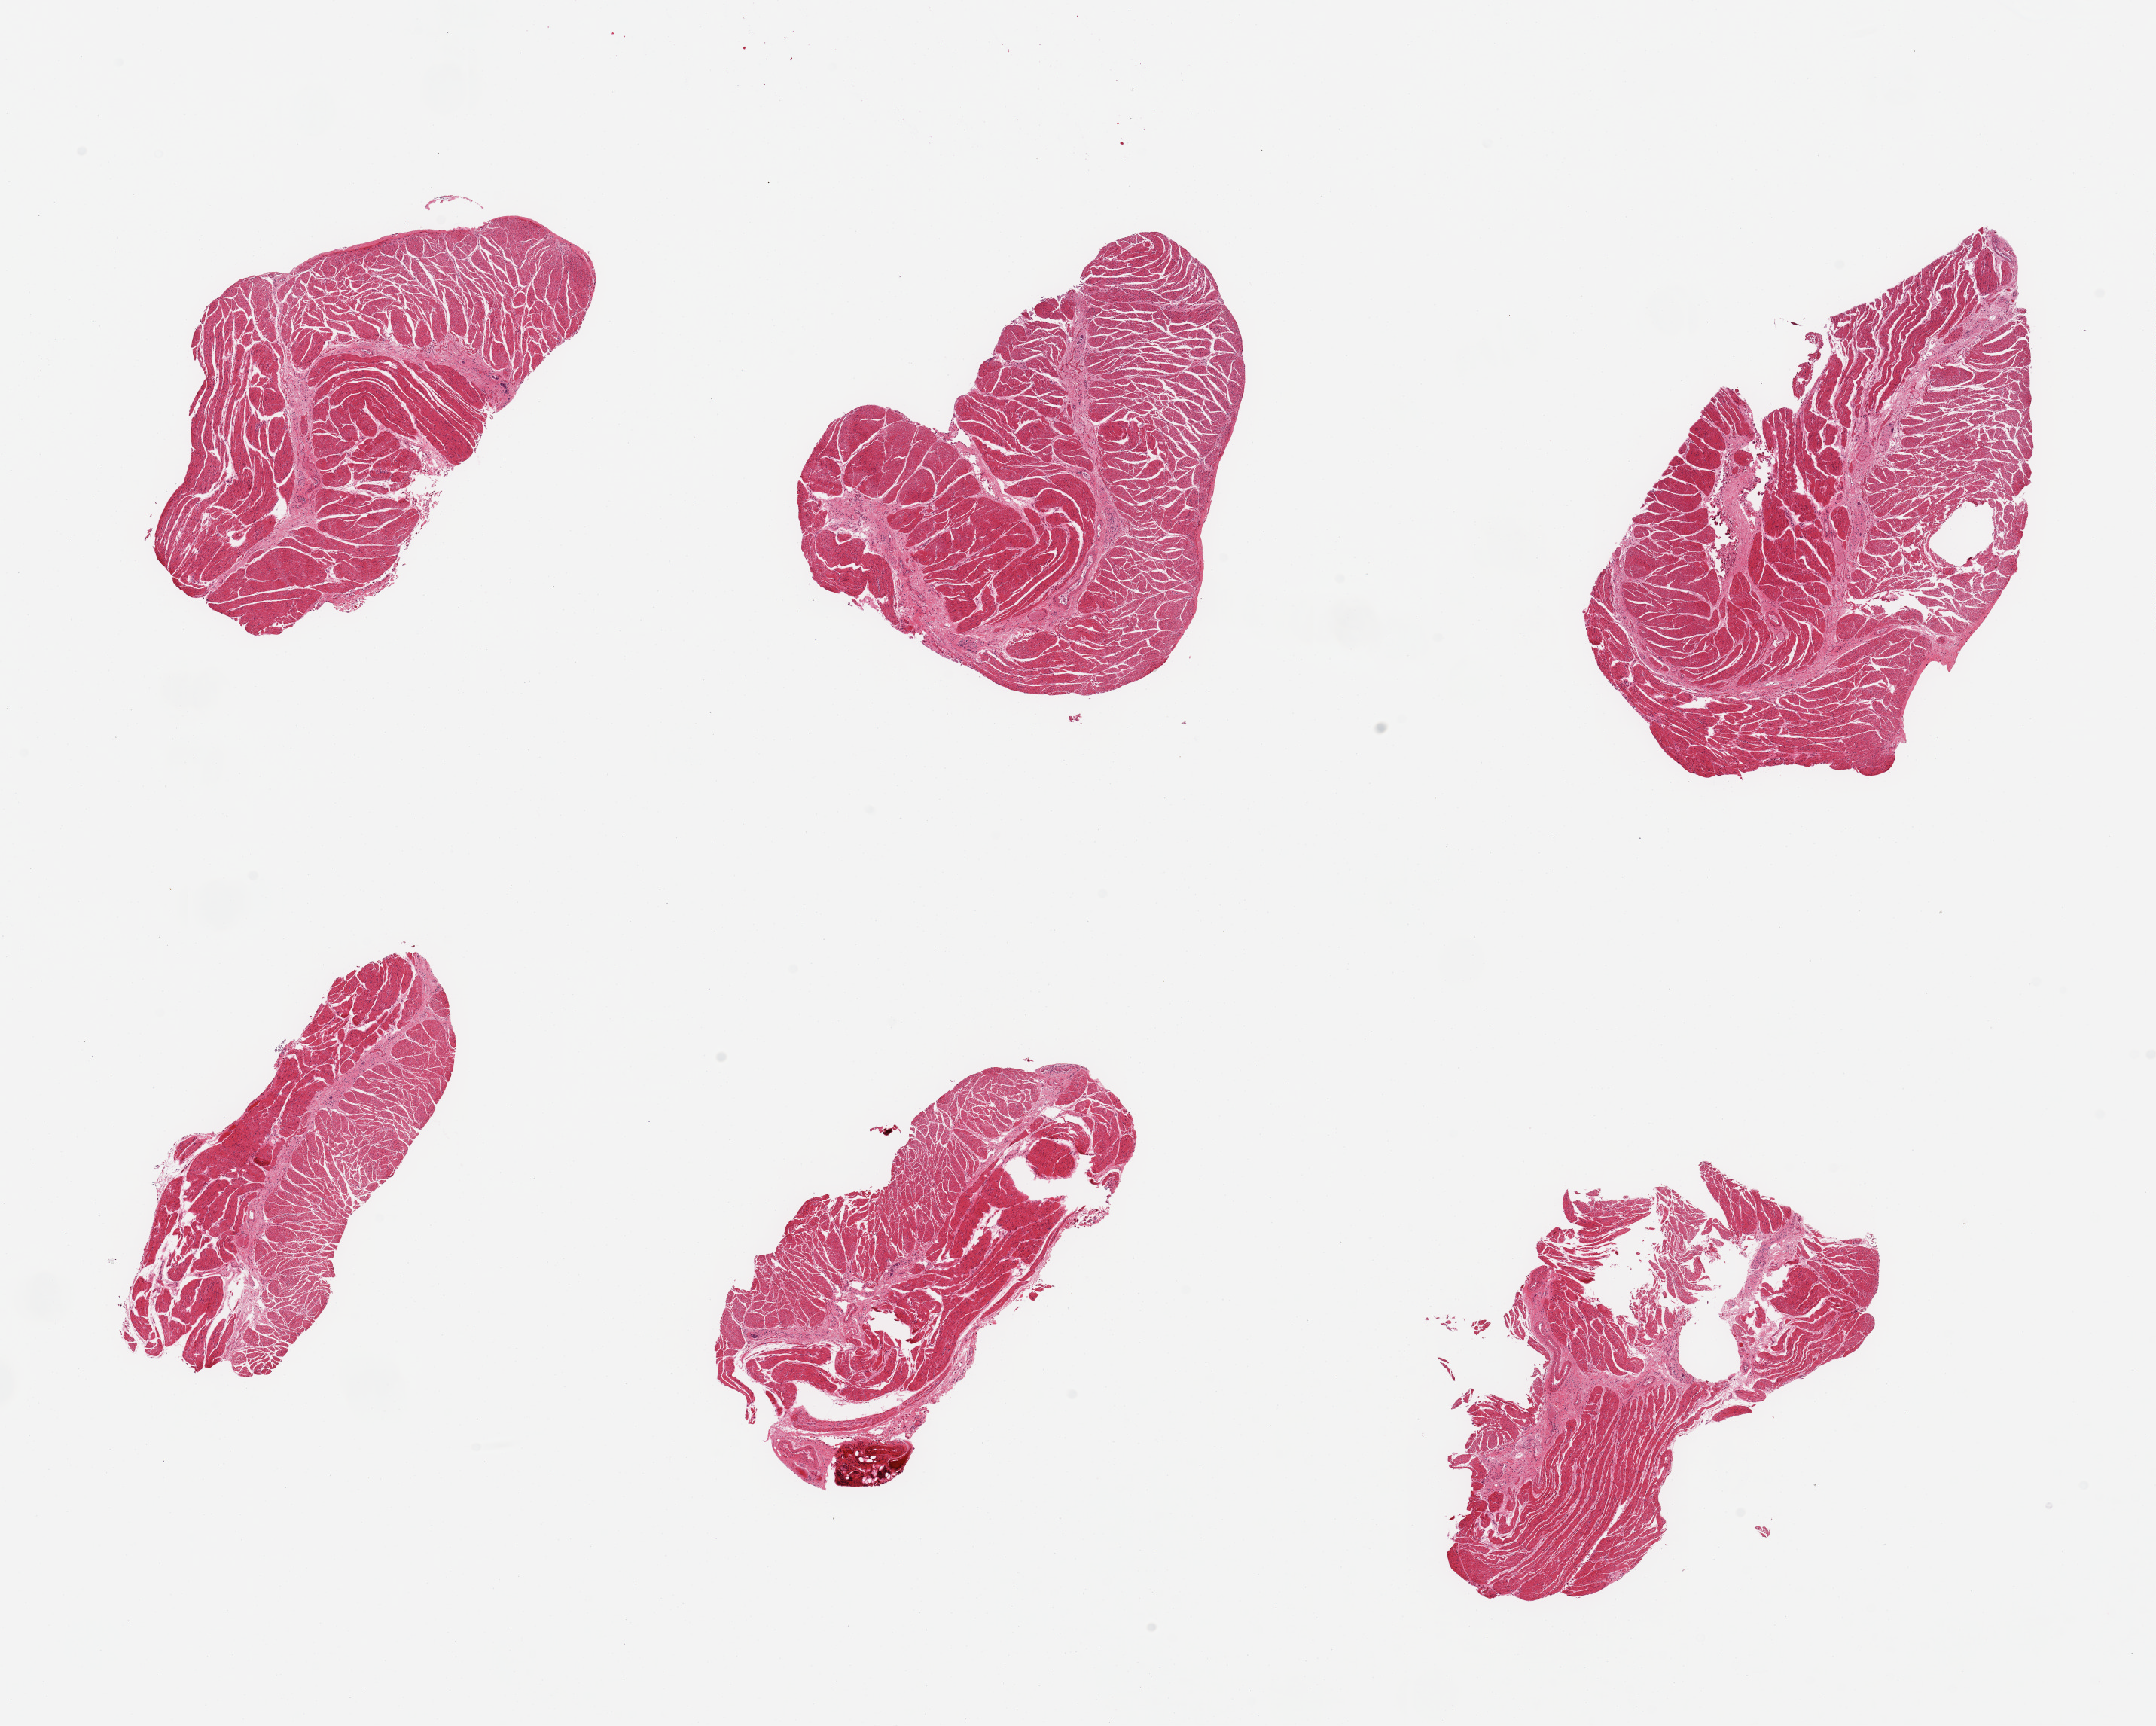
Hematoxylin and eosin (H&E) whole-slide image — whole scanned area (about 22.6 x 18.1 mm) shown as a low-resolution overview. PAXgene-fixed paraffin-embedded (PFPE) section. Section of esophageal muscle (target tissue). Donor tissue sample. Donor: male.
* reviewer comment on this tissue sample: 6 pieces, confirmed target muscularis